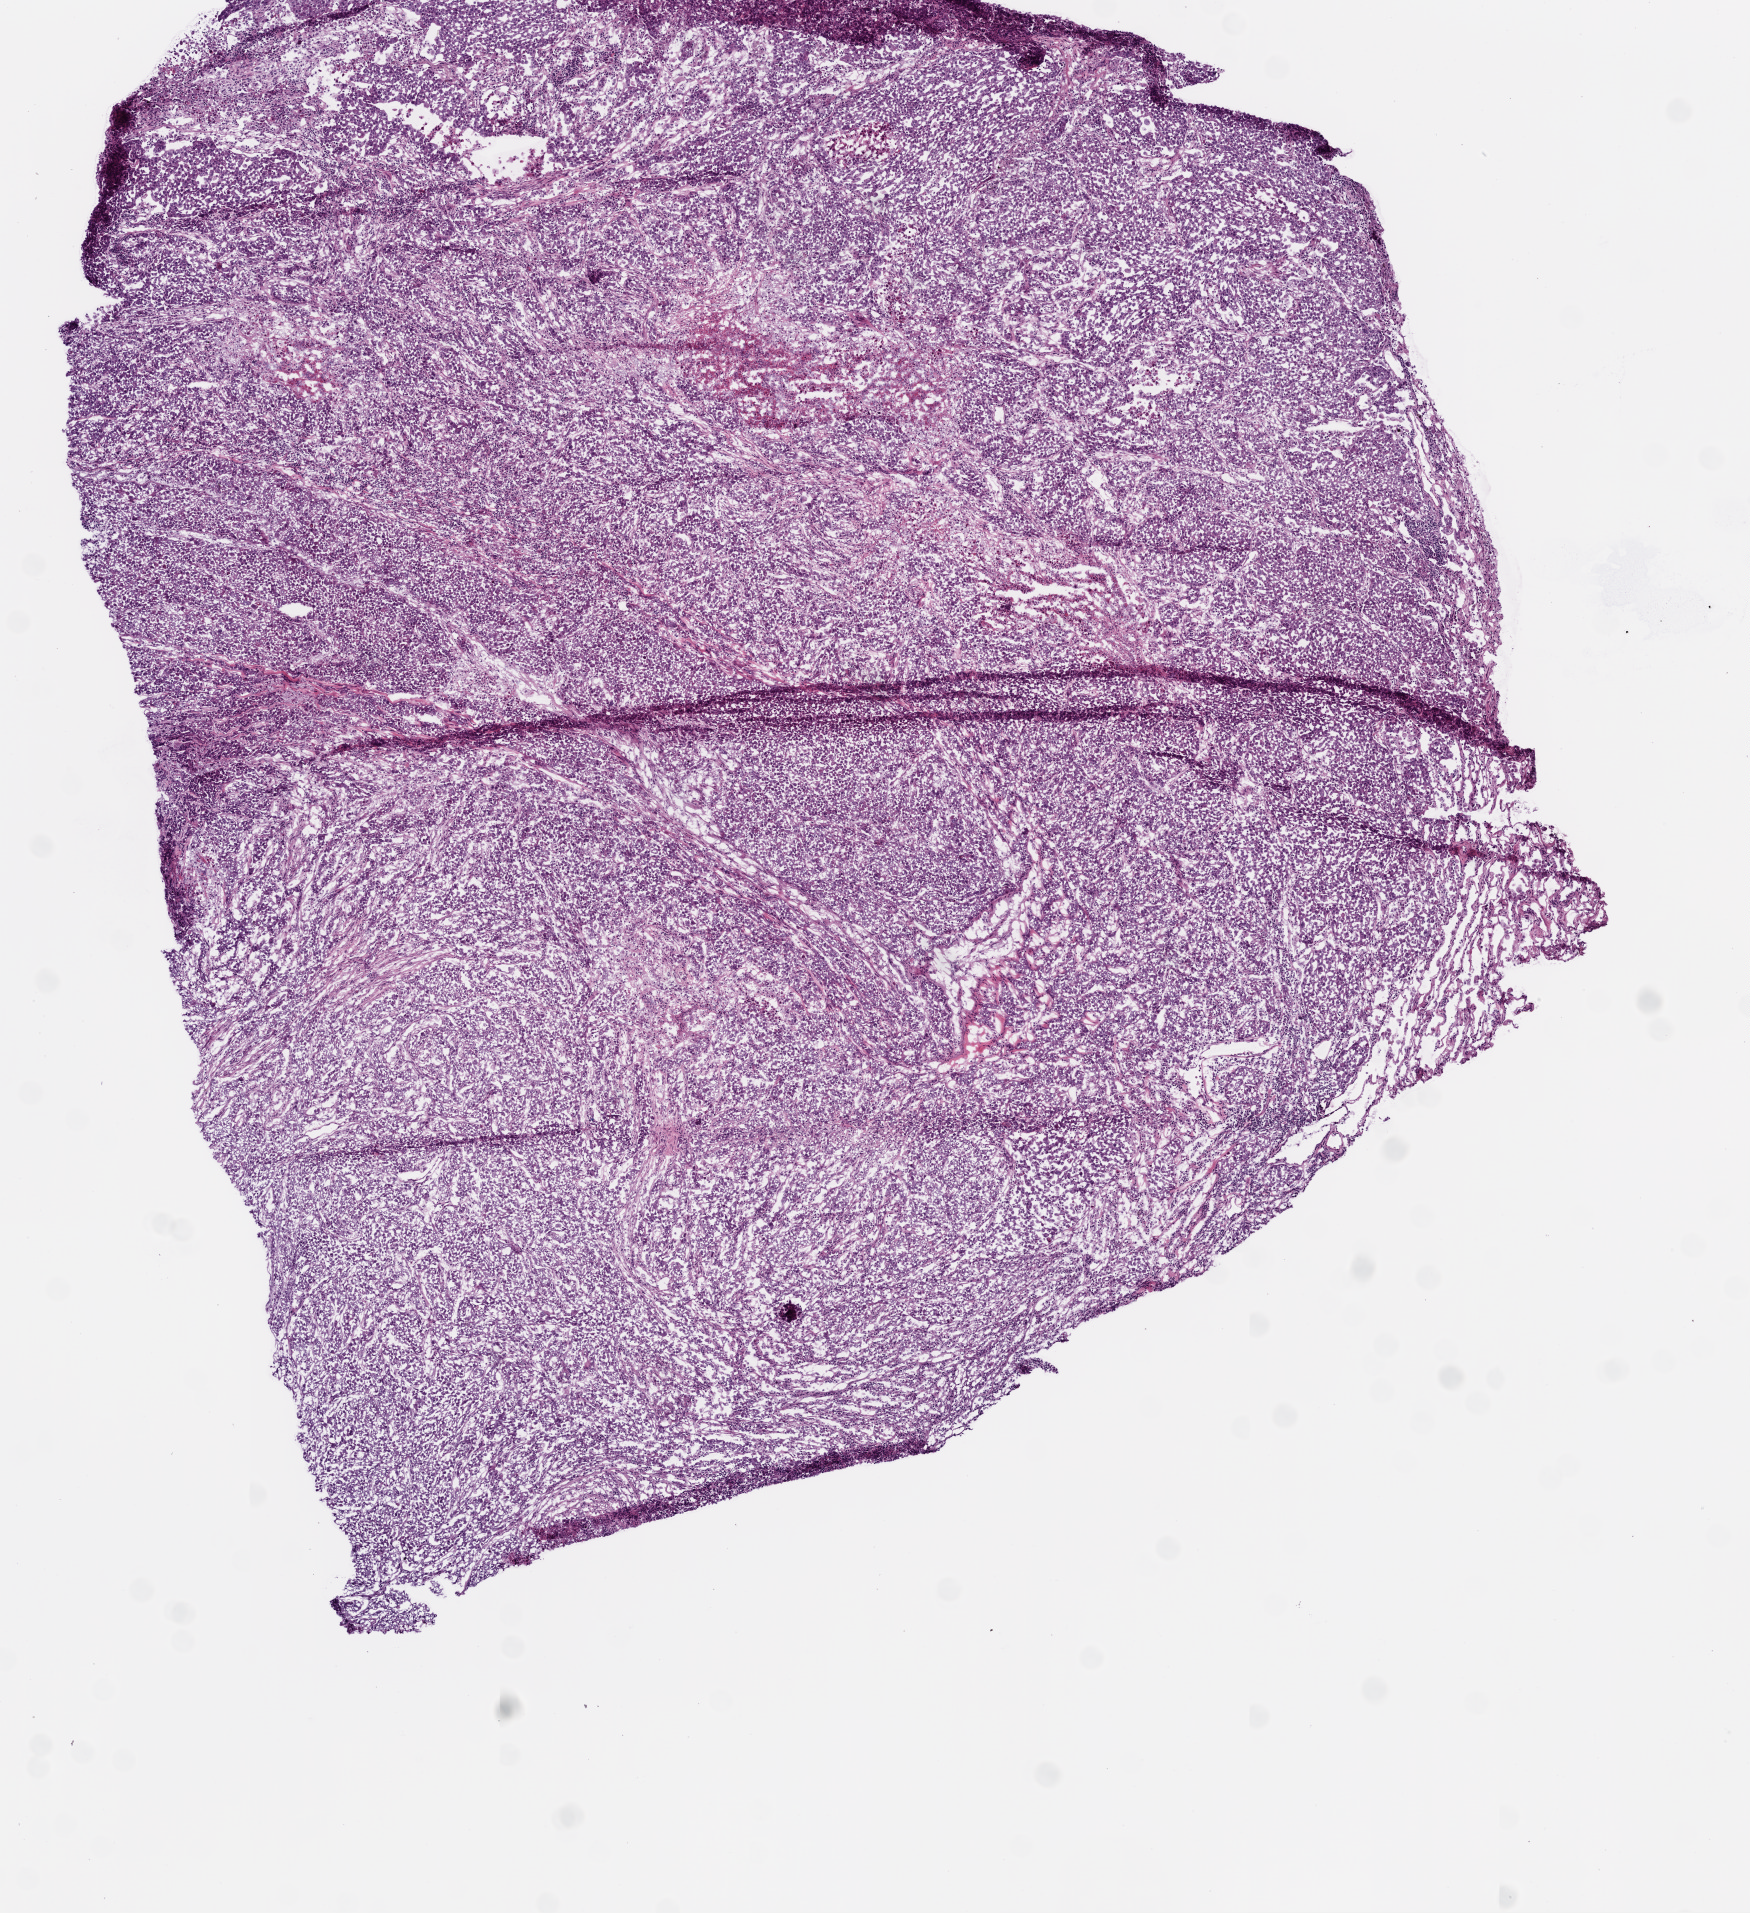
Whole-slide histology image, Hematoxylin and eosin (H&E) stained — shown as a low-resolution overview of the whole scanned area (about 7.0 x 7.7 mm); frozen section from the bottom of the tissue portion; sample: primary tumour, lung. Female patient; age at initial diagnosis 52 years. Composition of this section per pathologist review: tumour cells 95%, tumour nuclei 95%, normal cells 0%, stromal cells 0%, necrosis 5%.
Histologic diagnosis: Adenocarcinoma, NOS (upper lobe, lung). AJCC pathologic stage: IV.